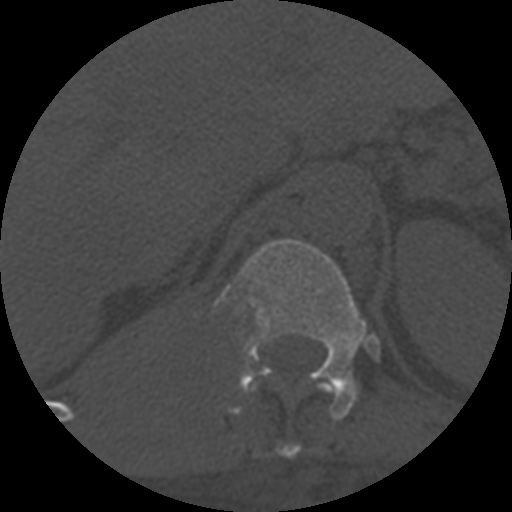
CT including the spine, one axial slice; one of 3 acquisitions stored at this slice position; bone window (W 1800 / L 400 HU); 1.25 mm slice thickness; 512 × 512 image matrix, field of view 160 × 160 mm. Patient age 55 years. Case-level facts recorded for this patient, not image findings: primary cancer: colon.
Outlined on this slice (semi-automatic segmentation, software-assisted and operator-edited):
- T11 vertebra: bounding box [x1, y1, x2, y2] px = [245, 381, 337, 458]
- T12 vertebra: [215, 239, 367, 420]